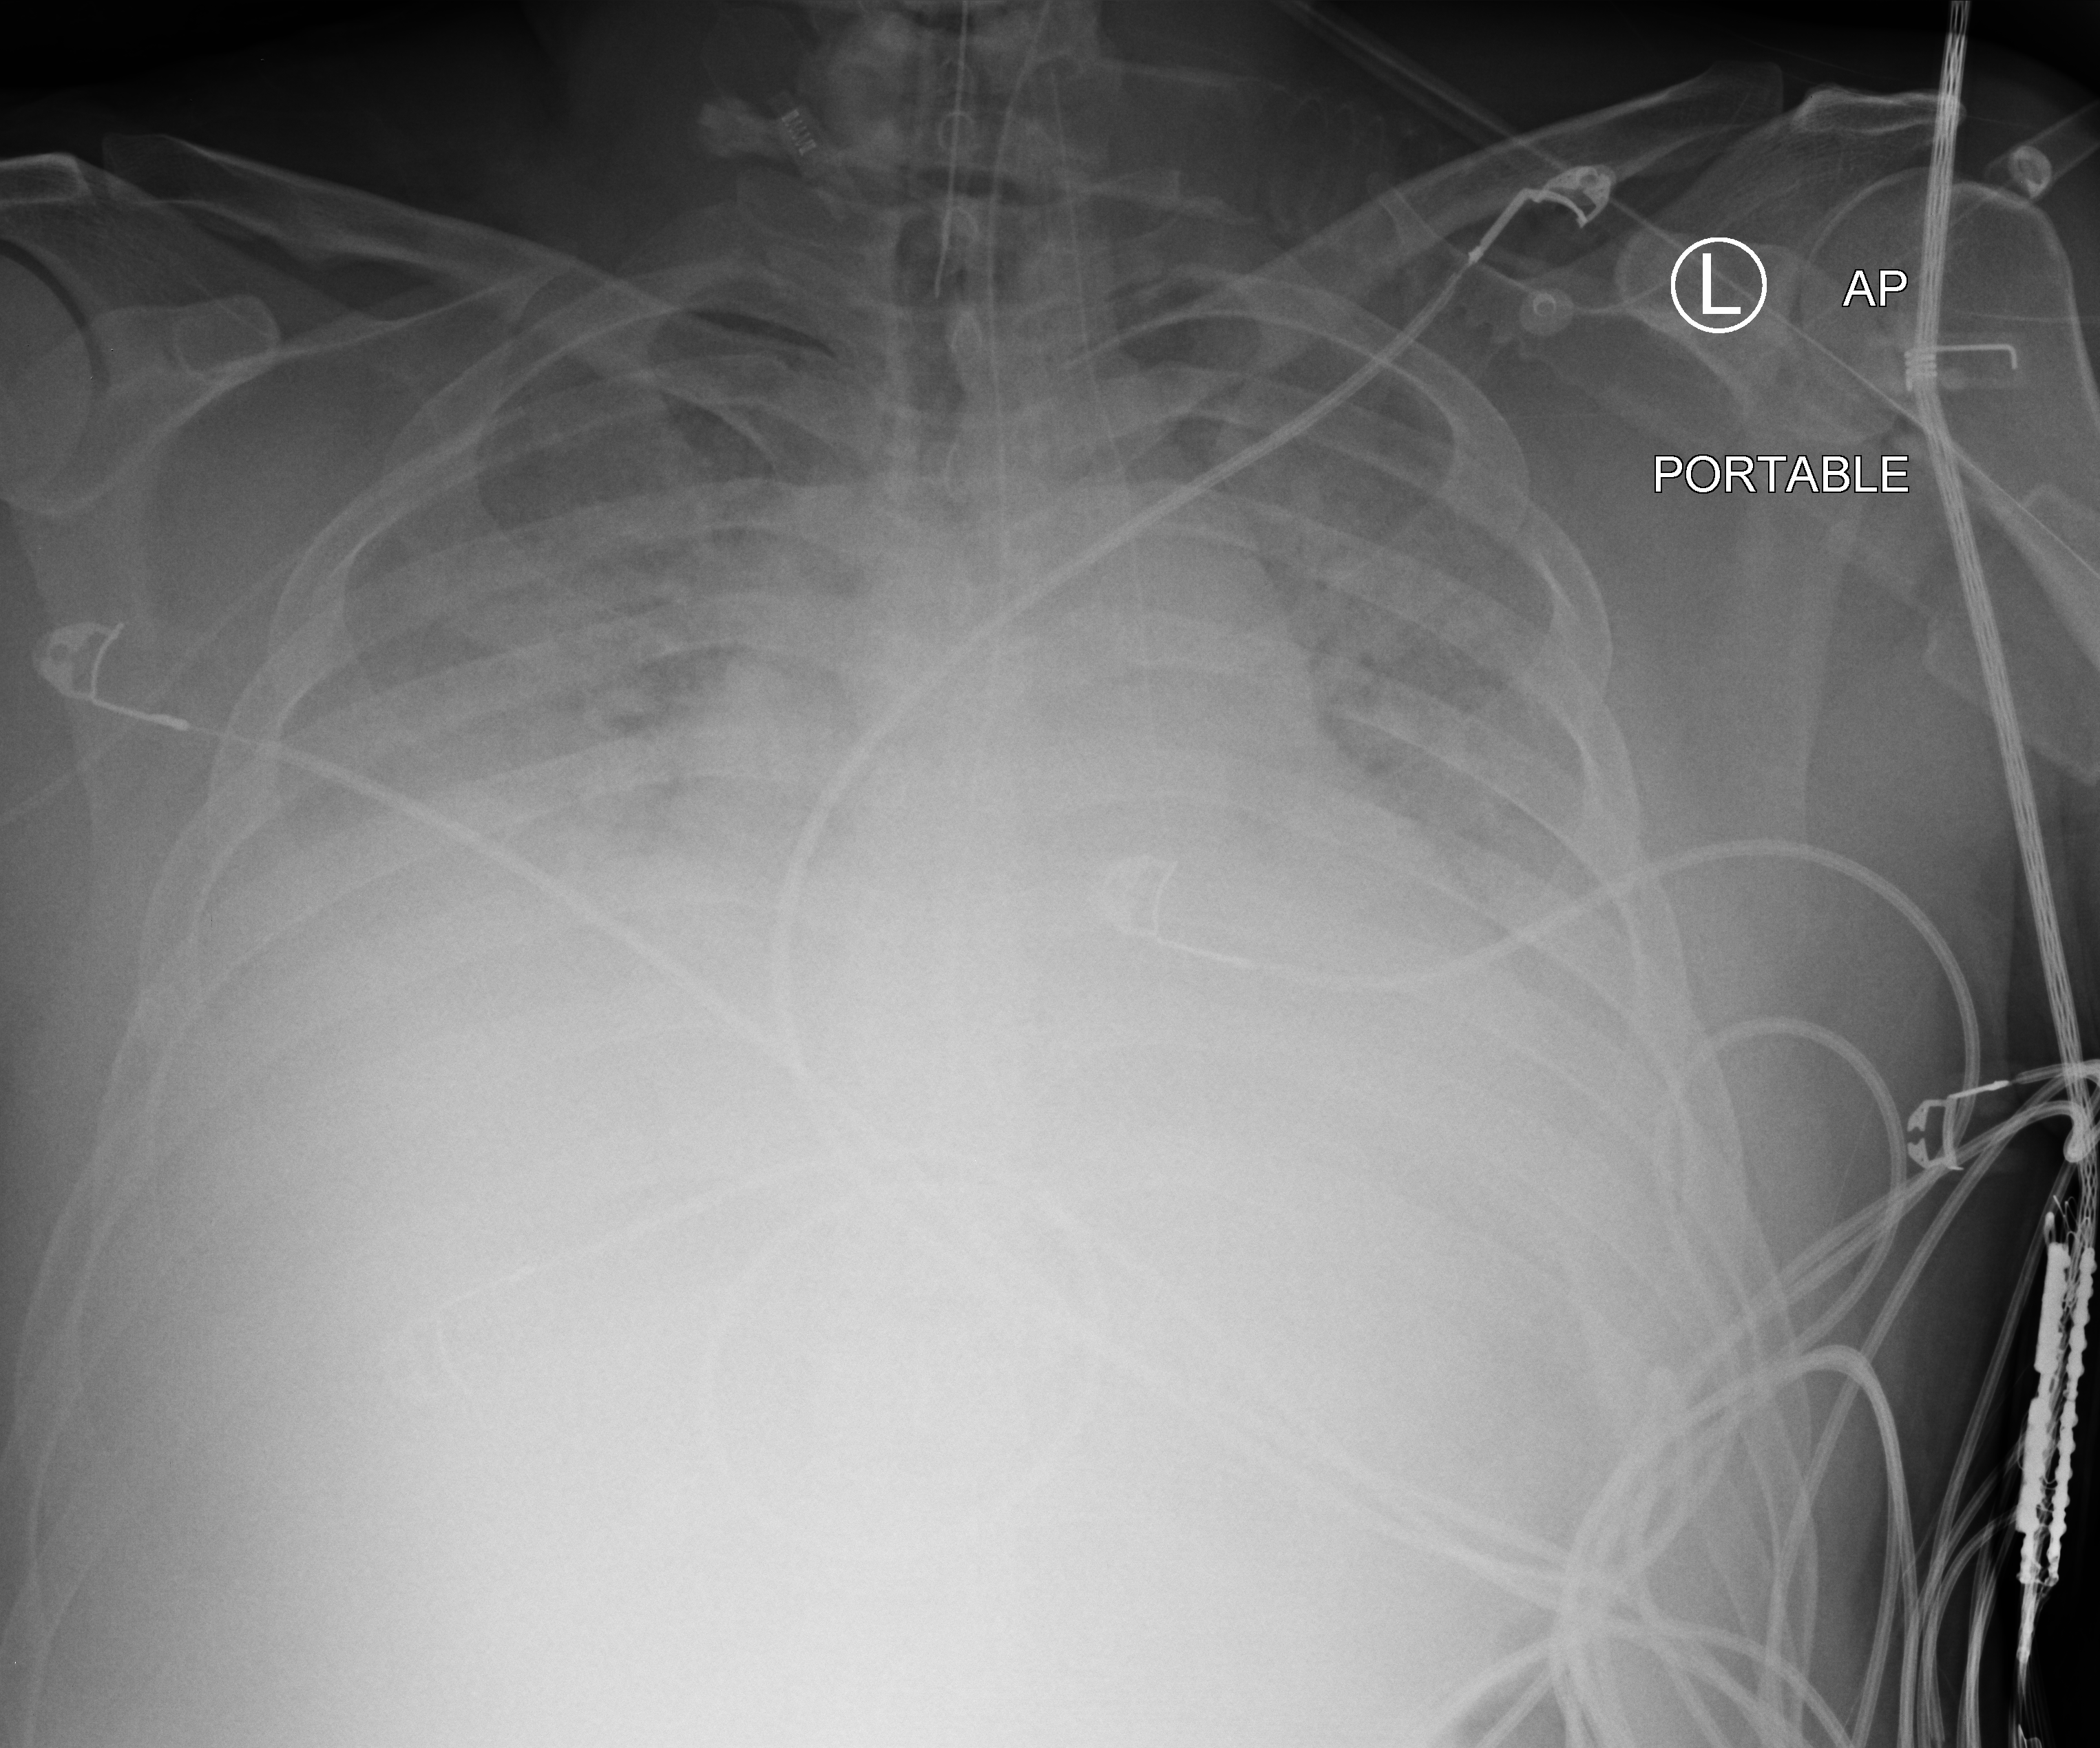
Portable chest radiograph; anteroposterior (AP) projection. Patient hospitalised with COVID-19; male, aged 18–59 years.
Hospital-stay facts (about this admission, not read from this image; timing relative to this image not recorded): admitted to intensive care during this hospital stay: yes; mechanically ventilated during this hospital stay: yes; length of hospital stay: 61 days.